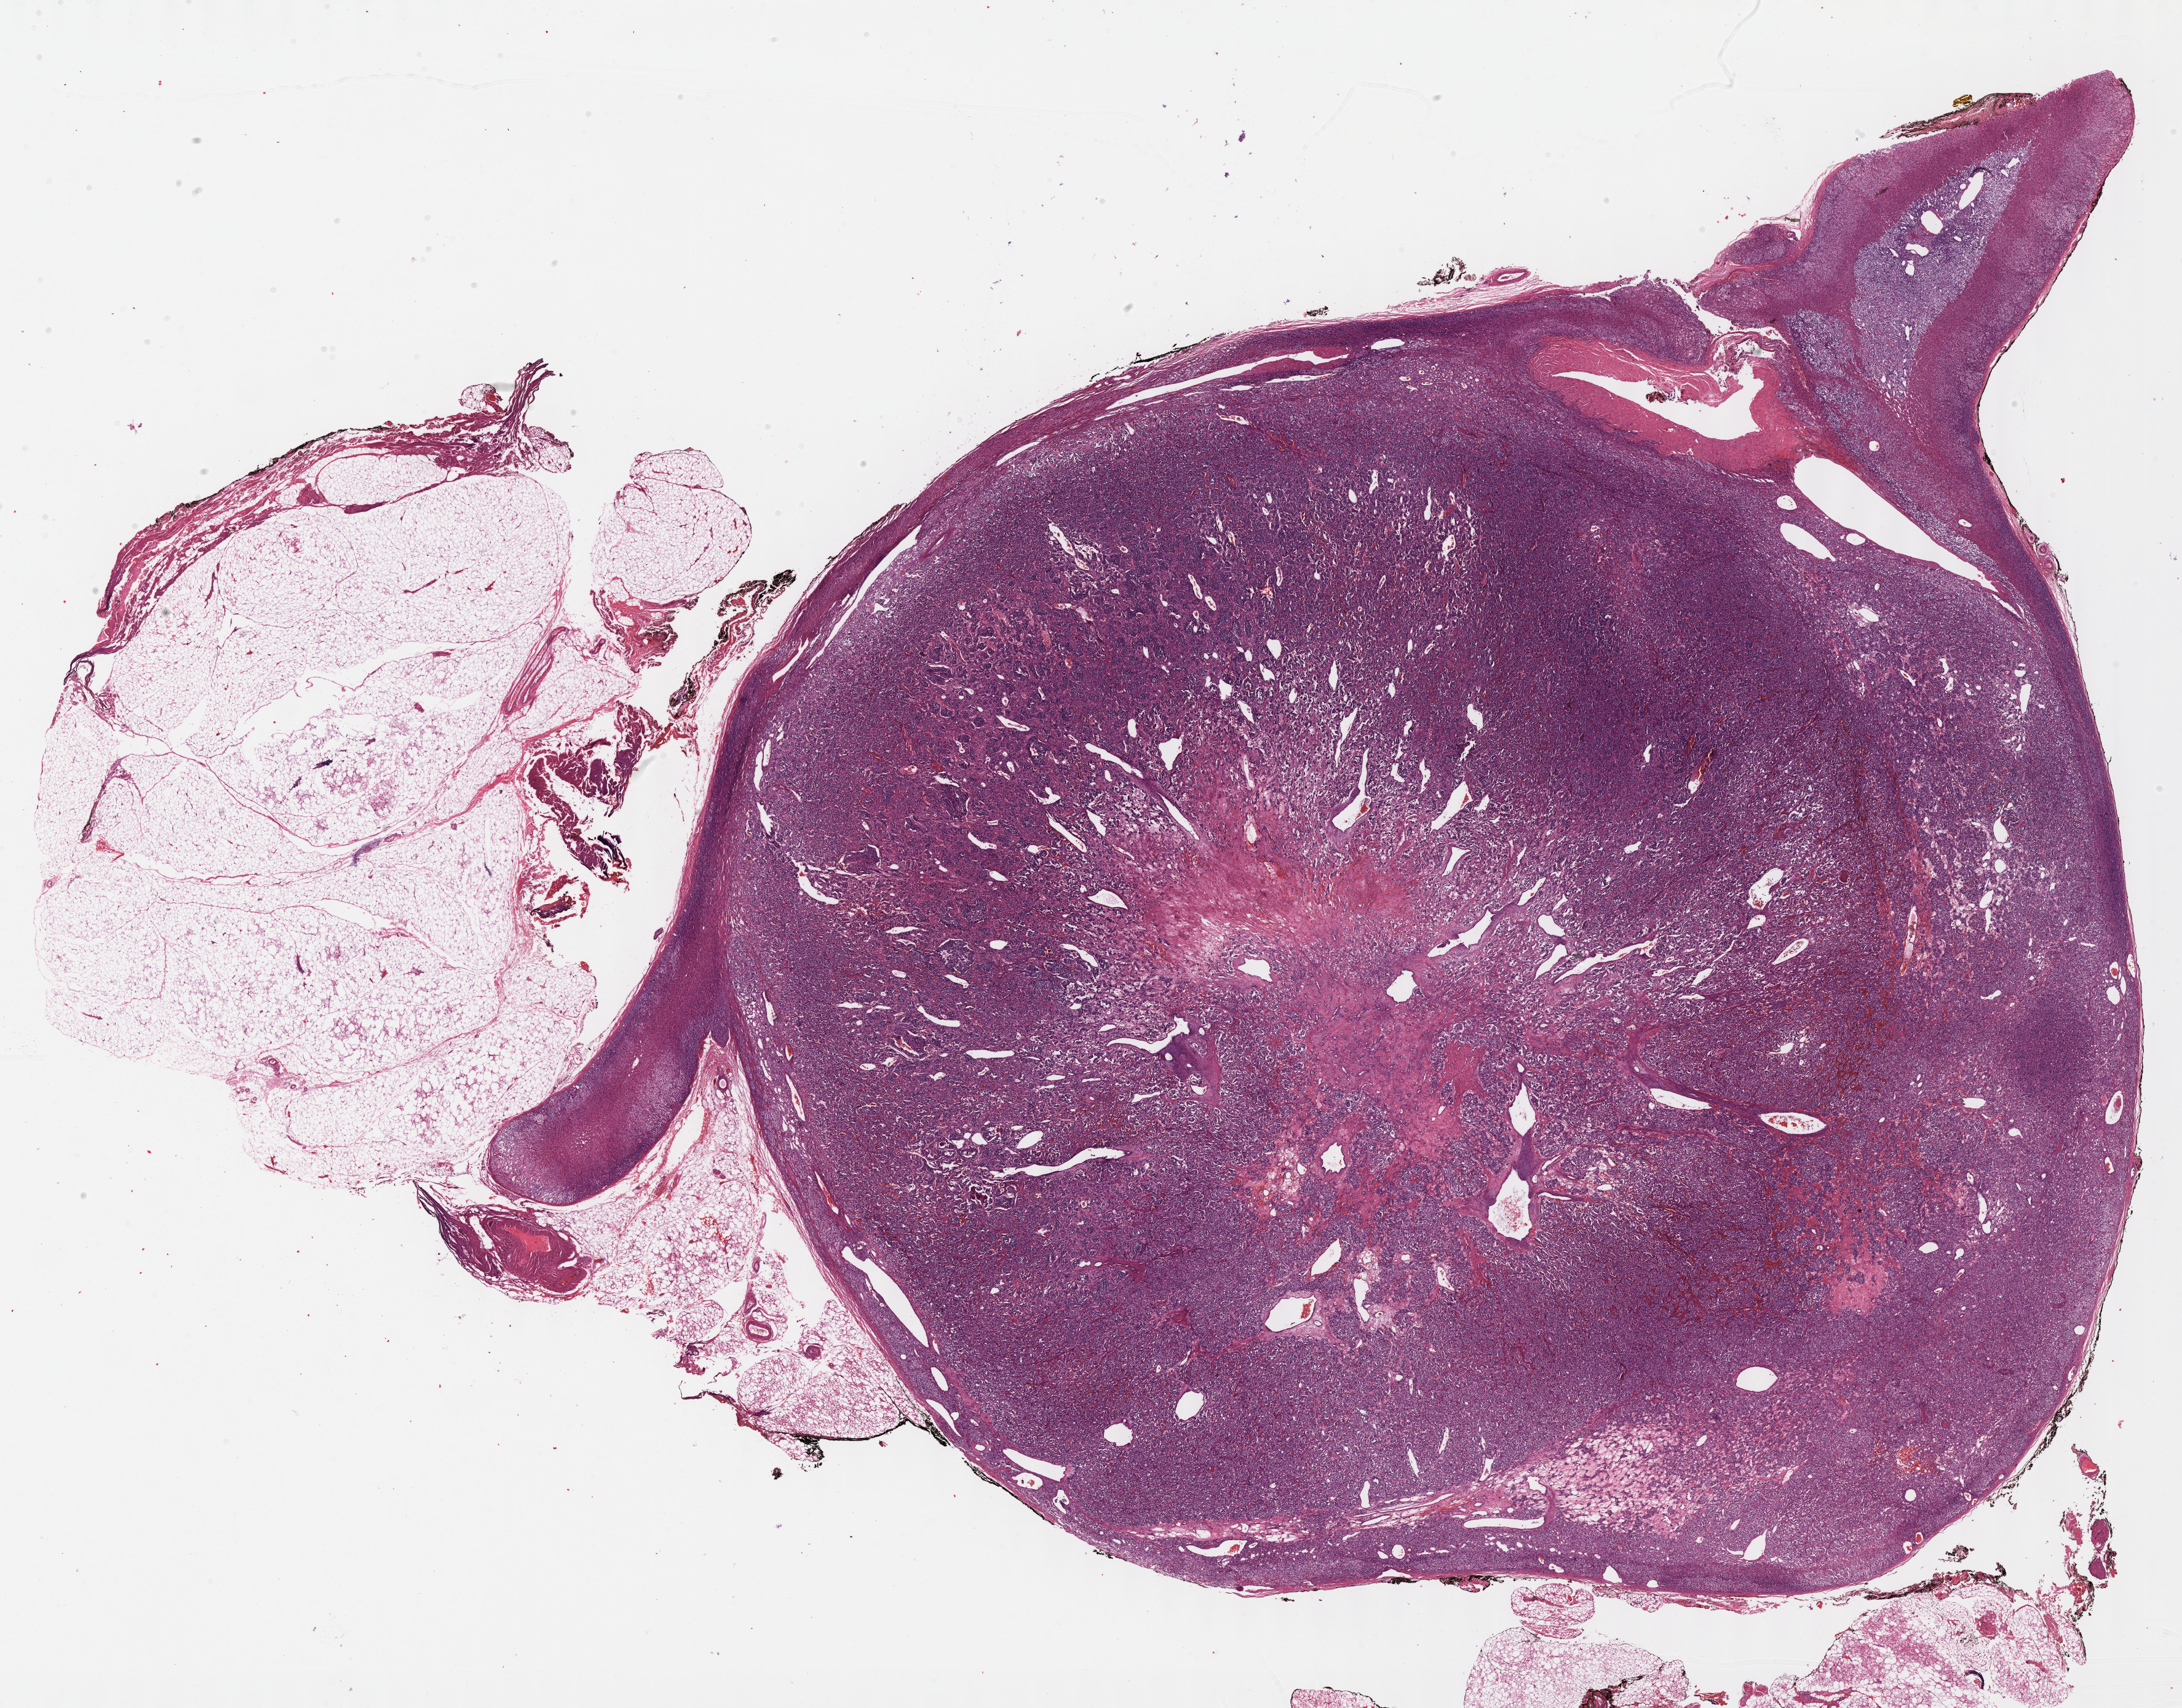
Whole-slide histology image, Hematoxylin and eosin (H&E) stained — low-resolution overview of the scanned area, about 28.7 x 22.4 mm (from a 40x scan), FFPE section, sample: primary tumour, adrenal gland. Female patient; age at initial diagnosis 19 years.
Pathologic diagnosis: Pheochromocytoma, NOS.